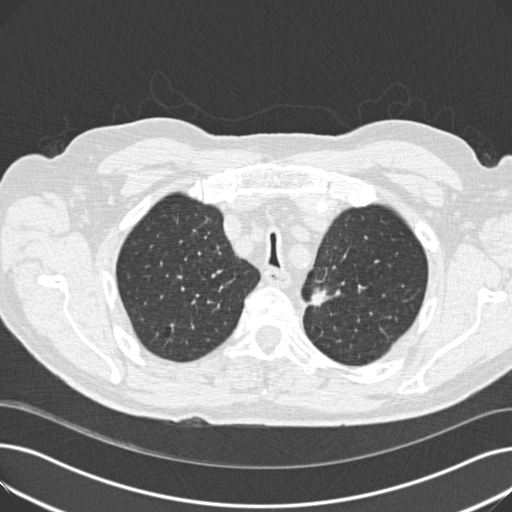
Chest CT (low-dose screening protocol), one axial image. Third annual screen. Lung window (W 1500 / L -600 HU). 2 mm slice thickness. Standard (soft-tissue) reconstruction kernel (B30f). Male, age 70 years at enrolment. Current smoker at enrolment.
Lesion marked by an expert reader, bounding box [x1, y1, x2, y2] px = [297, 273, 340, 315]. The screening reader recorded 2 non-calcified nodules or masses ≥4 mm on this exam; which of them this box marks is not recorded. Later outcome: lung cancer diagnosed 175 days after this screen — mixed cell adenocarcinoma, left upper lobe, poorly differentiated (G3), stage IIB (AJCC 6th edition), 17 mm at pathology.